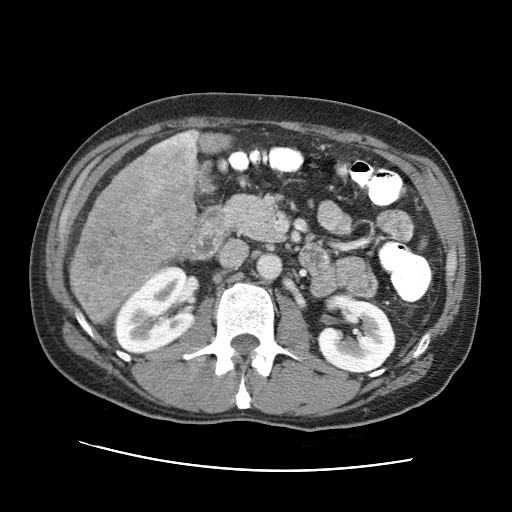
Contrast-enhanced abdominal CT (liver protocol), one axial slice. Position 27 of 95 along the scan axis. One of 2 acquisitions stored at this slice position. Soft-tissue window (W 400 / L 40 HU). 2.5 mm slice thickness. 512 × 512 image matrix, field of view 360 × 360 mm. From the clinical record (not read from this slice): diagnosis: hepatocellular carcinoma (patient treated with transarterial chemoembolisation; whether this scan precedes or follows treatment is not stated here); TNM stage (as recorded): Stage-IVA; Child-Pugh class: A; tumour differentiation: moderately differentiated; tumour nodularity: multinodular.
Outlined on this slice (semi-automatically segmented with operator editing):
- liver parenchyma outside the tumour (the mass and vessels are separate outlines, so this box may not span the whole liver): box from (x=70, y=131) to (x=228, y=286) px
- mass: (x=70, y=130)–(x=196, y=326)